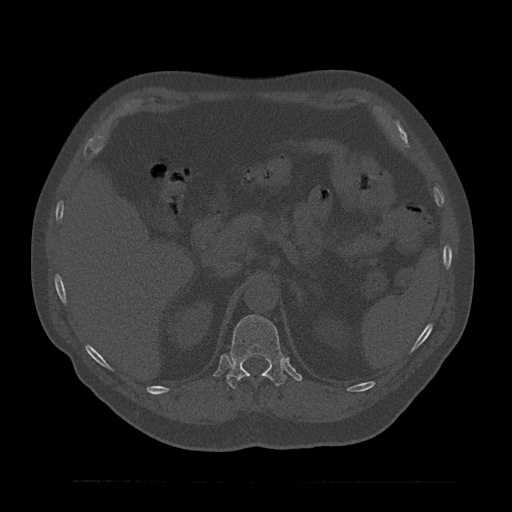
CT including the spine, one axial slice; position 240 of 797 along the scan axis; reconstruction kernel Br40s/3; 120 kVp; bone window (W 1800 / L 400 HU); 0.5 mm slice thickness; 512 × 512 image matrix, field of view 430 × 430 mm. Patient: male, 61 years. Case-level facts recorded for this patient, not image findings: primary cancer: prostate.
Structures marked on this image (semi-automatically segmented with operator editing):
- T12 vertebra: bounding box [x1, y1, x2, y2] px = [227, 315, 287, 389]